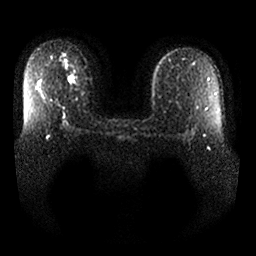
Breast MRI, one axial slice. Slice 23 of 25 in the series (ordered by position). Diffusion-weighted series; image 2 of 4 stored at this slice position (different b-values; order by instance number). 1.5 T. 256 × 256 image matrix, field of view 360 × 360 mm. Female patient.
Structures marked on this image (manually delineated by an expert):
- tumour on diffusion-weighted imaging: bounding box (x1, y1, x2, y2) in pixels: (68, 74, 78, 84)